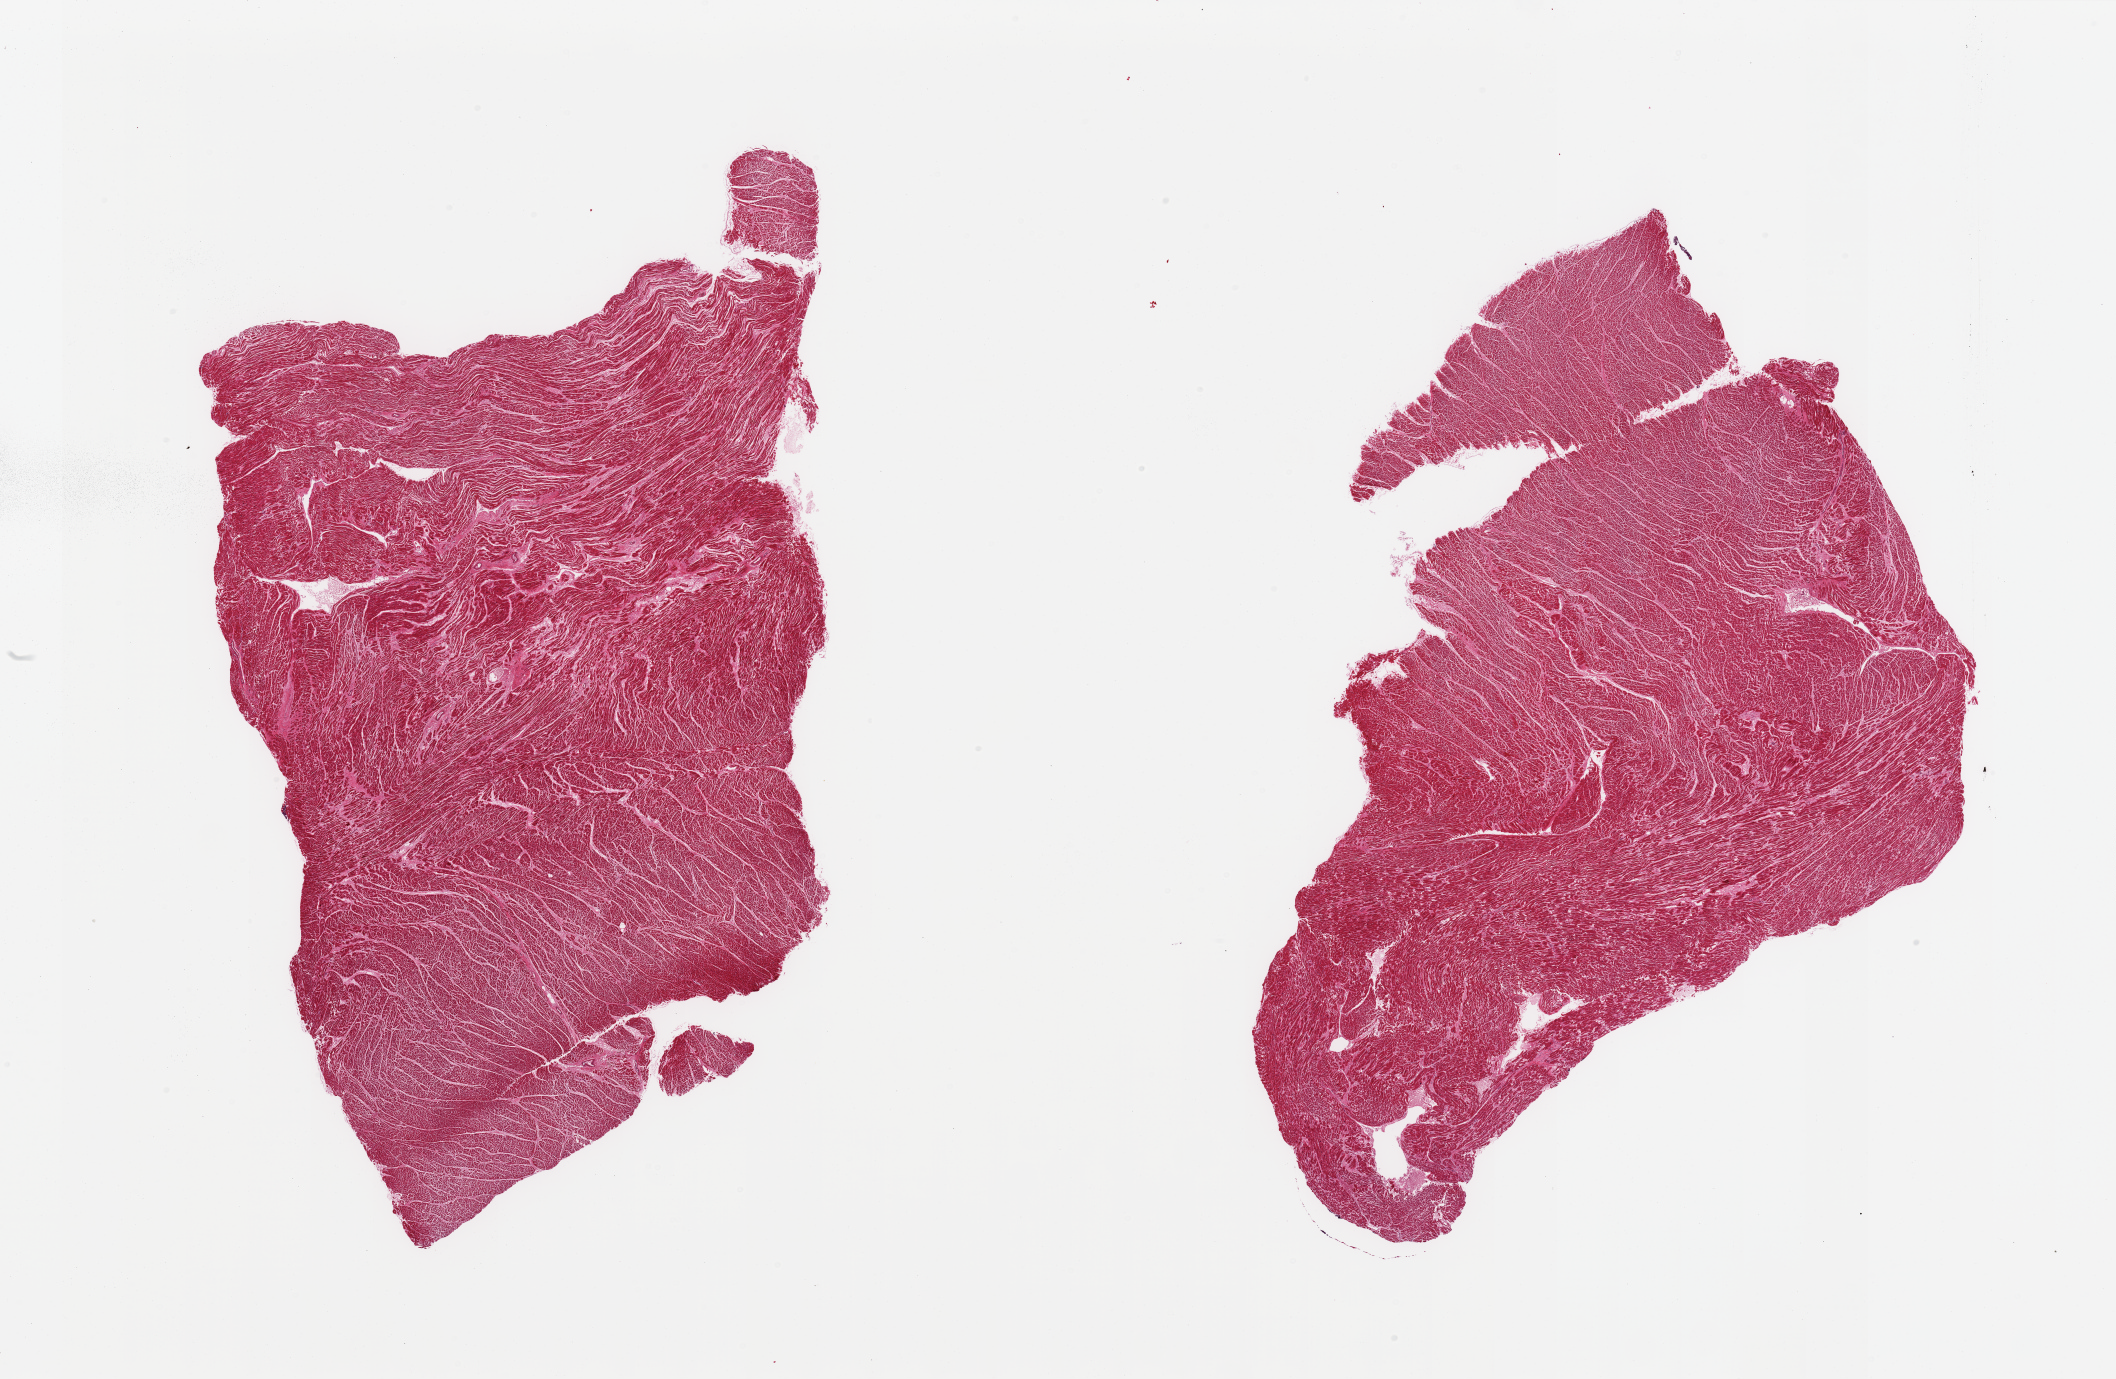
Whole-slide image, haematoxylin and eosin stain, brightfield, shown as a low-resolution overview of the whole scanned area (about 33.5 x 21.8 mm, acquisition: 20x scan); PAXgene-fixed paraffin-embedded (PFPE) section; sampled site (target tissue): heart; tissue donor sample. Donor: male.
- review note (as recorded): 2 pieces; myocardium with interstitial fibrosis and focal scarring